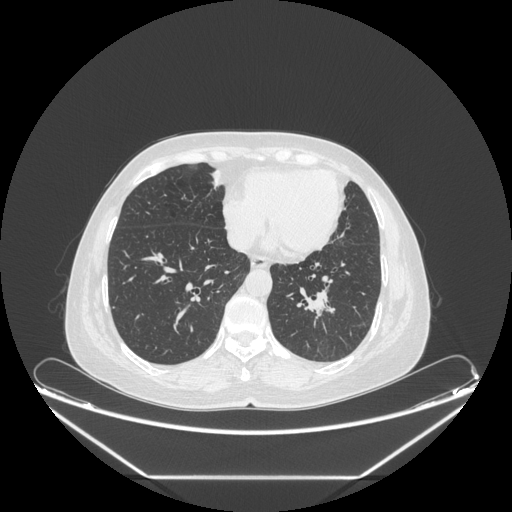
Chest CT, one axial slice. Position 84 of 241 along the scan axis. Reconstruction kernel STANDARD. Lung window (W 1500 / L -600 HU). 1.25 mm slice thickness. 512 × 512 image matrix, field of view 451 × 451 mm. Patient: female, 63 years. Case-level facts recorded for this patient, not image findings: clinical TNM (as recorded): T1c N0 M0.
Outlined on this slice (bounding box drawn by a radiologist):
- lung tumour (recorded histology: adenocarcinoma): bounding box [x1, y1, x2, y2] px = [301, 285, 335, 328]